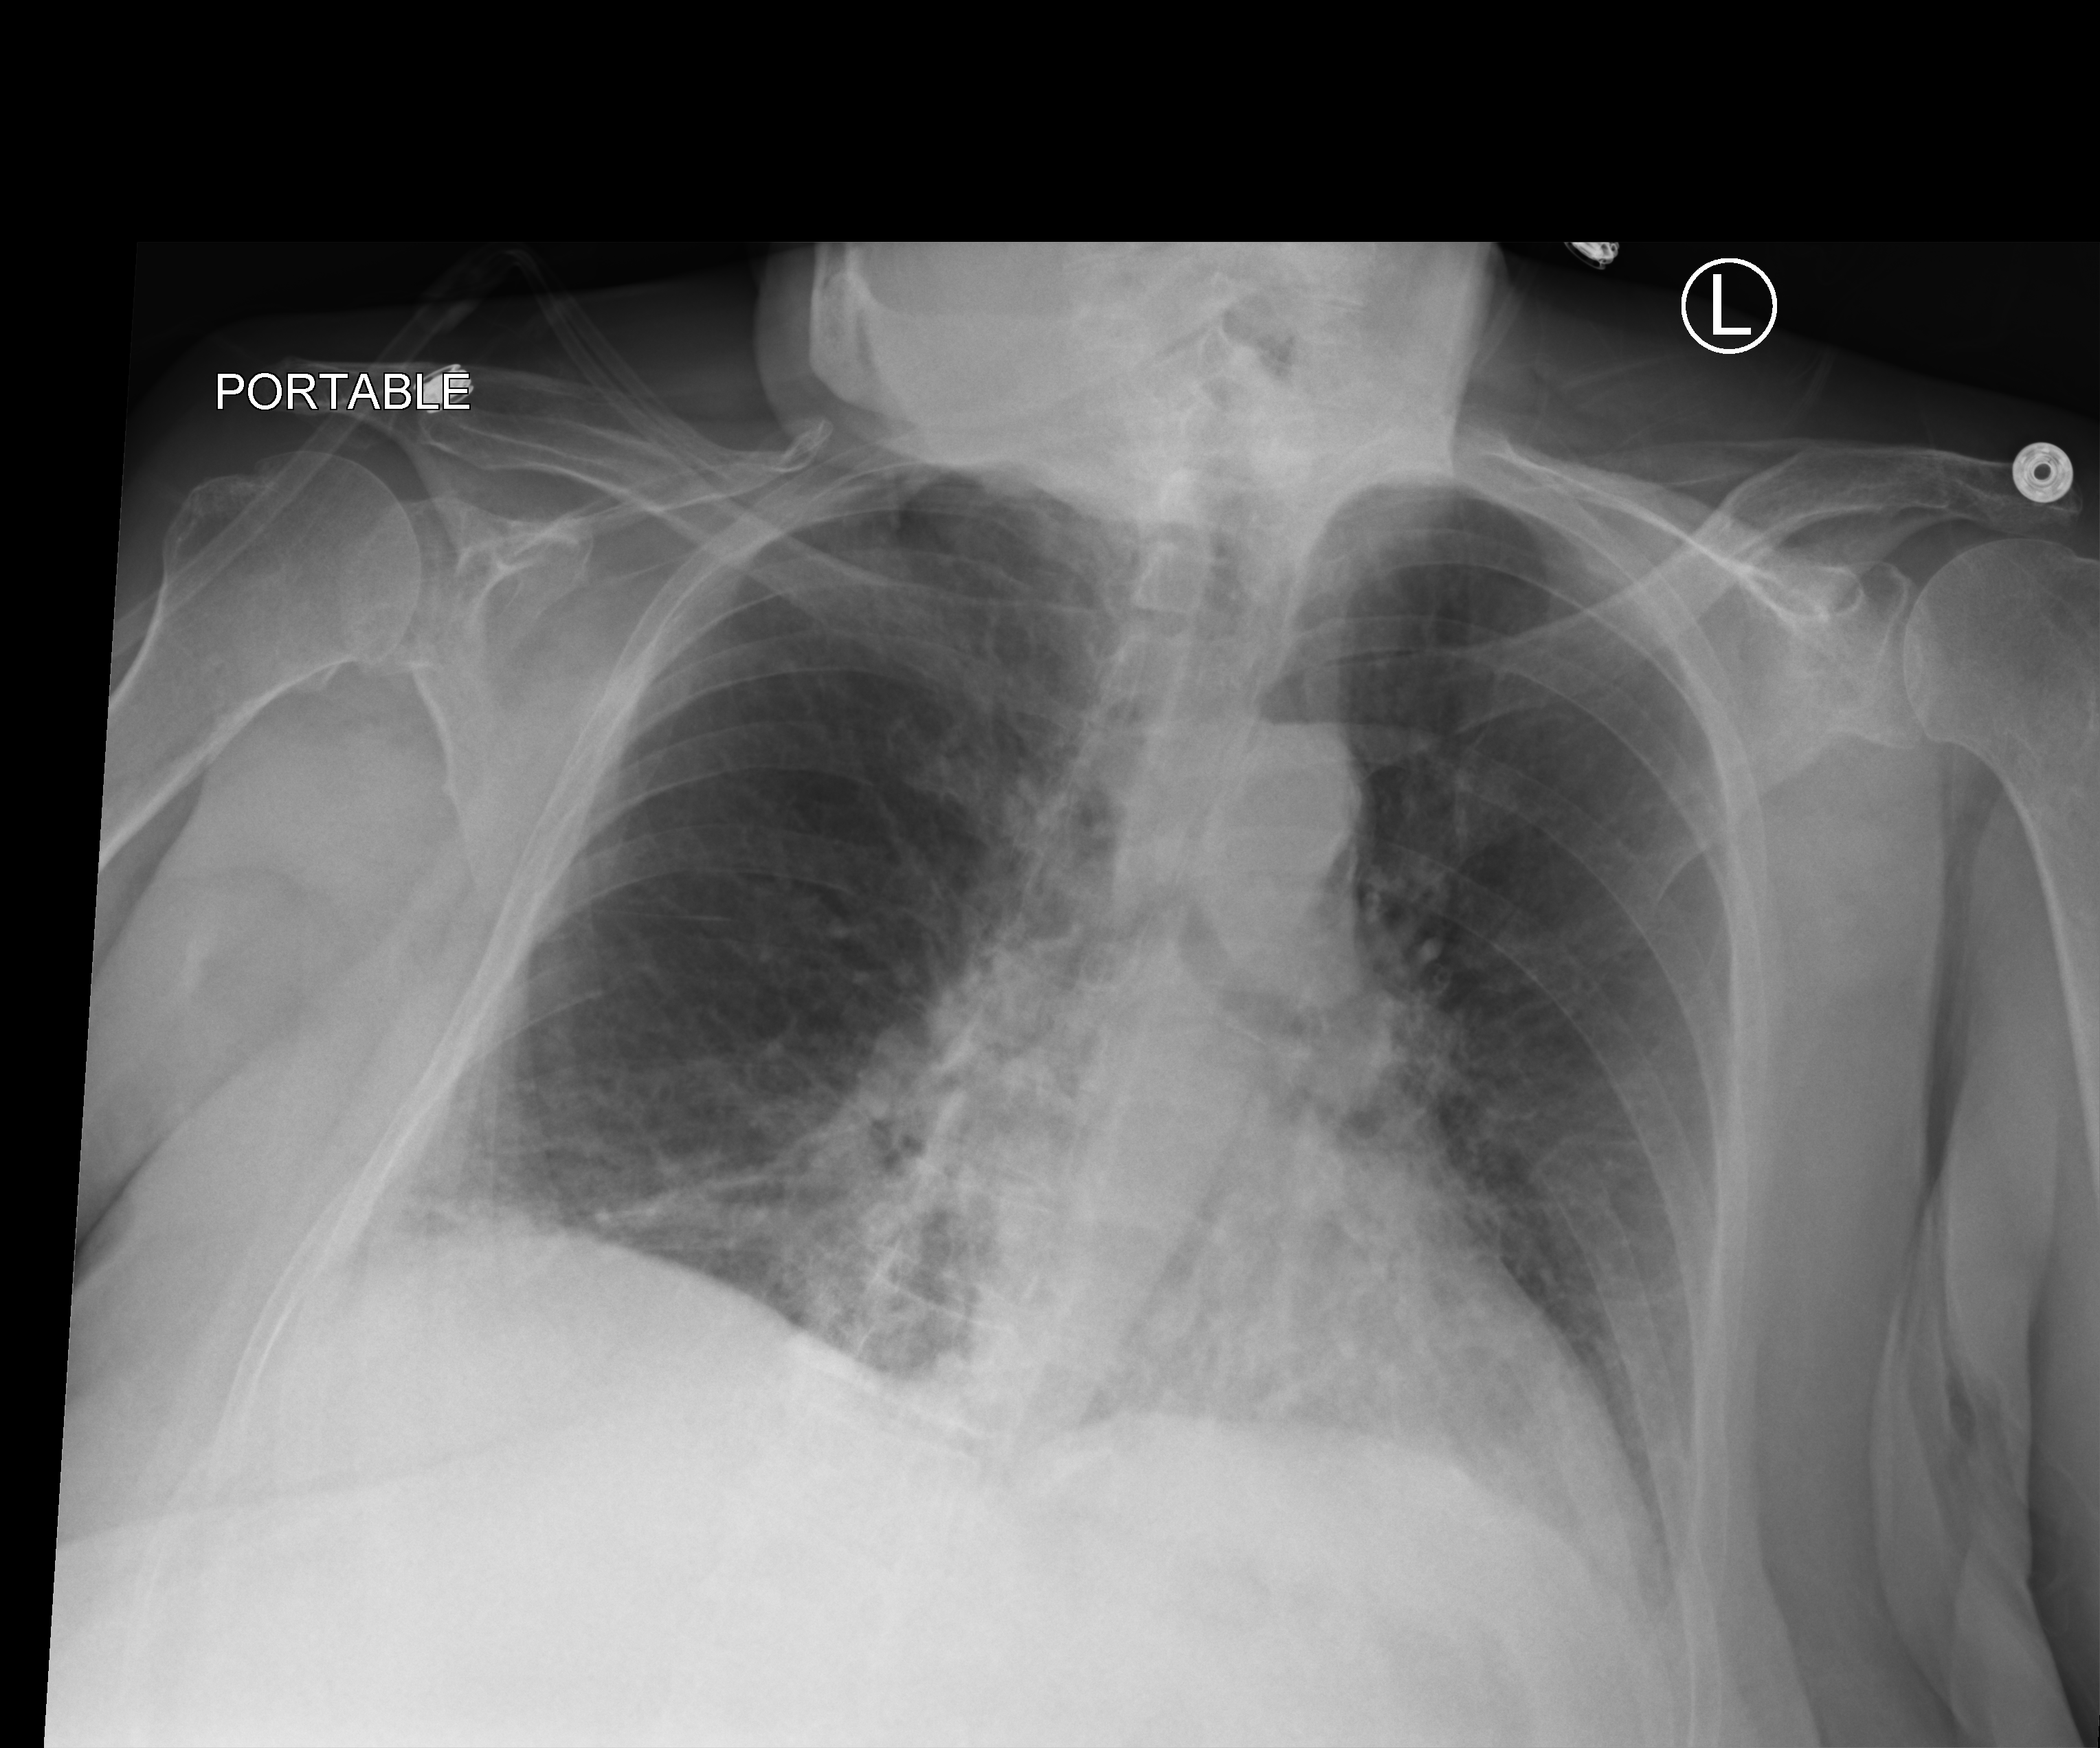
Chest X-ray (portable), anteroposterior (AP) projection. Patient hospitalised with COVID-19; female, aged 75–90 years.
Admission-level facts for this patient (not findings on this image; timing relative to this image not recorded):
- COPD (admission record): yes